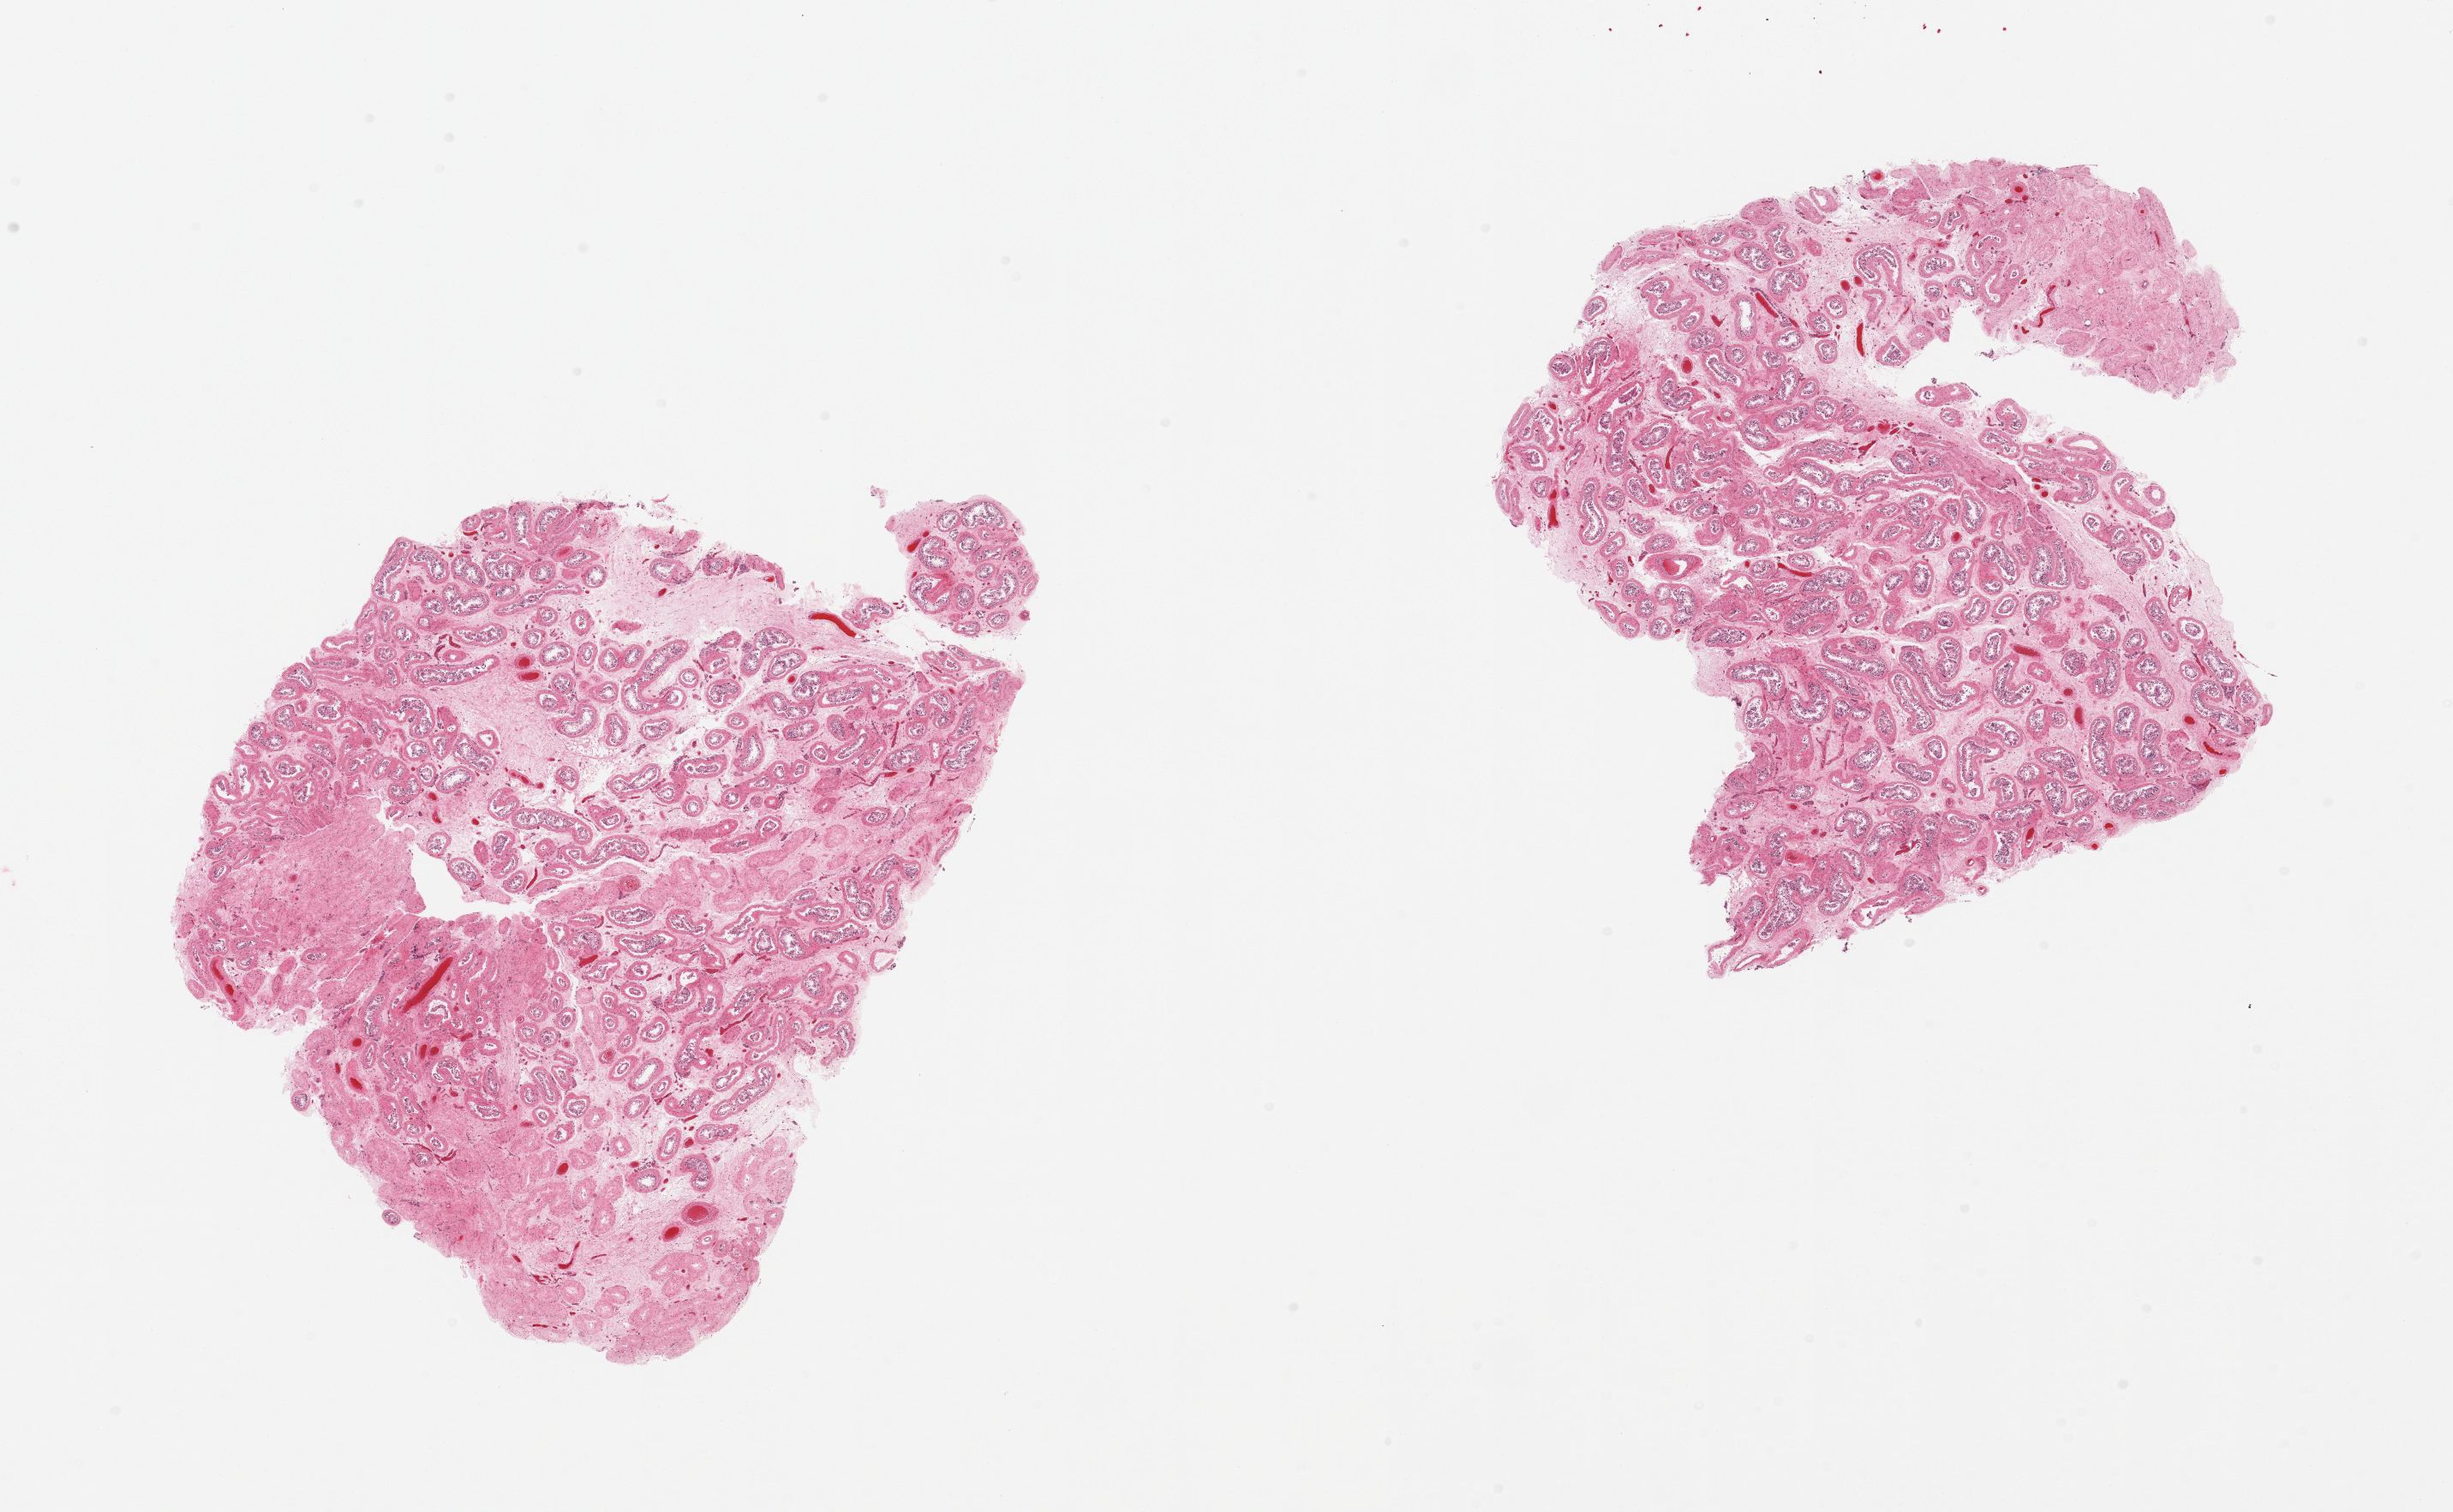
Hematoxylin and eosin (H&E) whole-slide image, shown as a low-resolution overview of the whole scanned area (about 22.6 x 14.0 mm, slide scanned at 20x), PAXgene-fixed paraffin-embedded (PFPE) section, sampled site (target tissue): testis, donor tissue sample.
* pathologist's review note for this sample: 2 pieces, markedly reduced spermatogenesis, Serotoli only